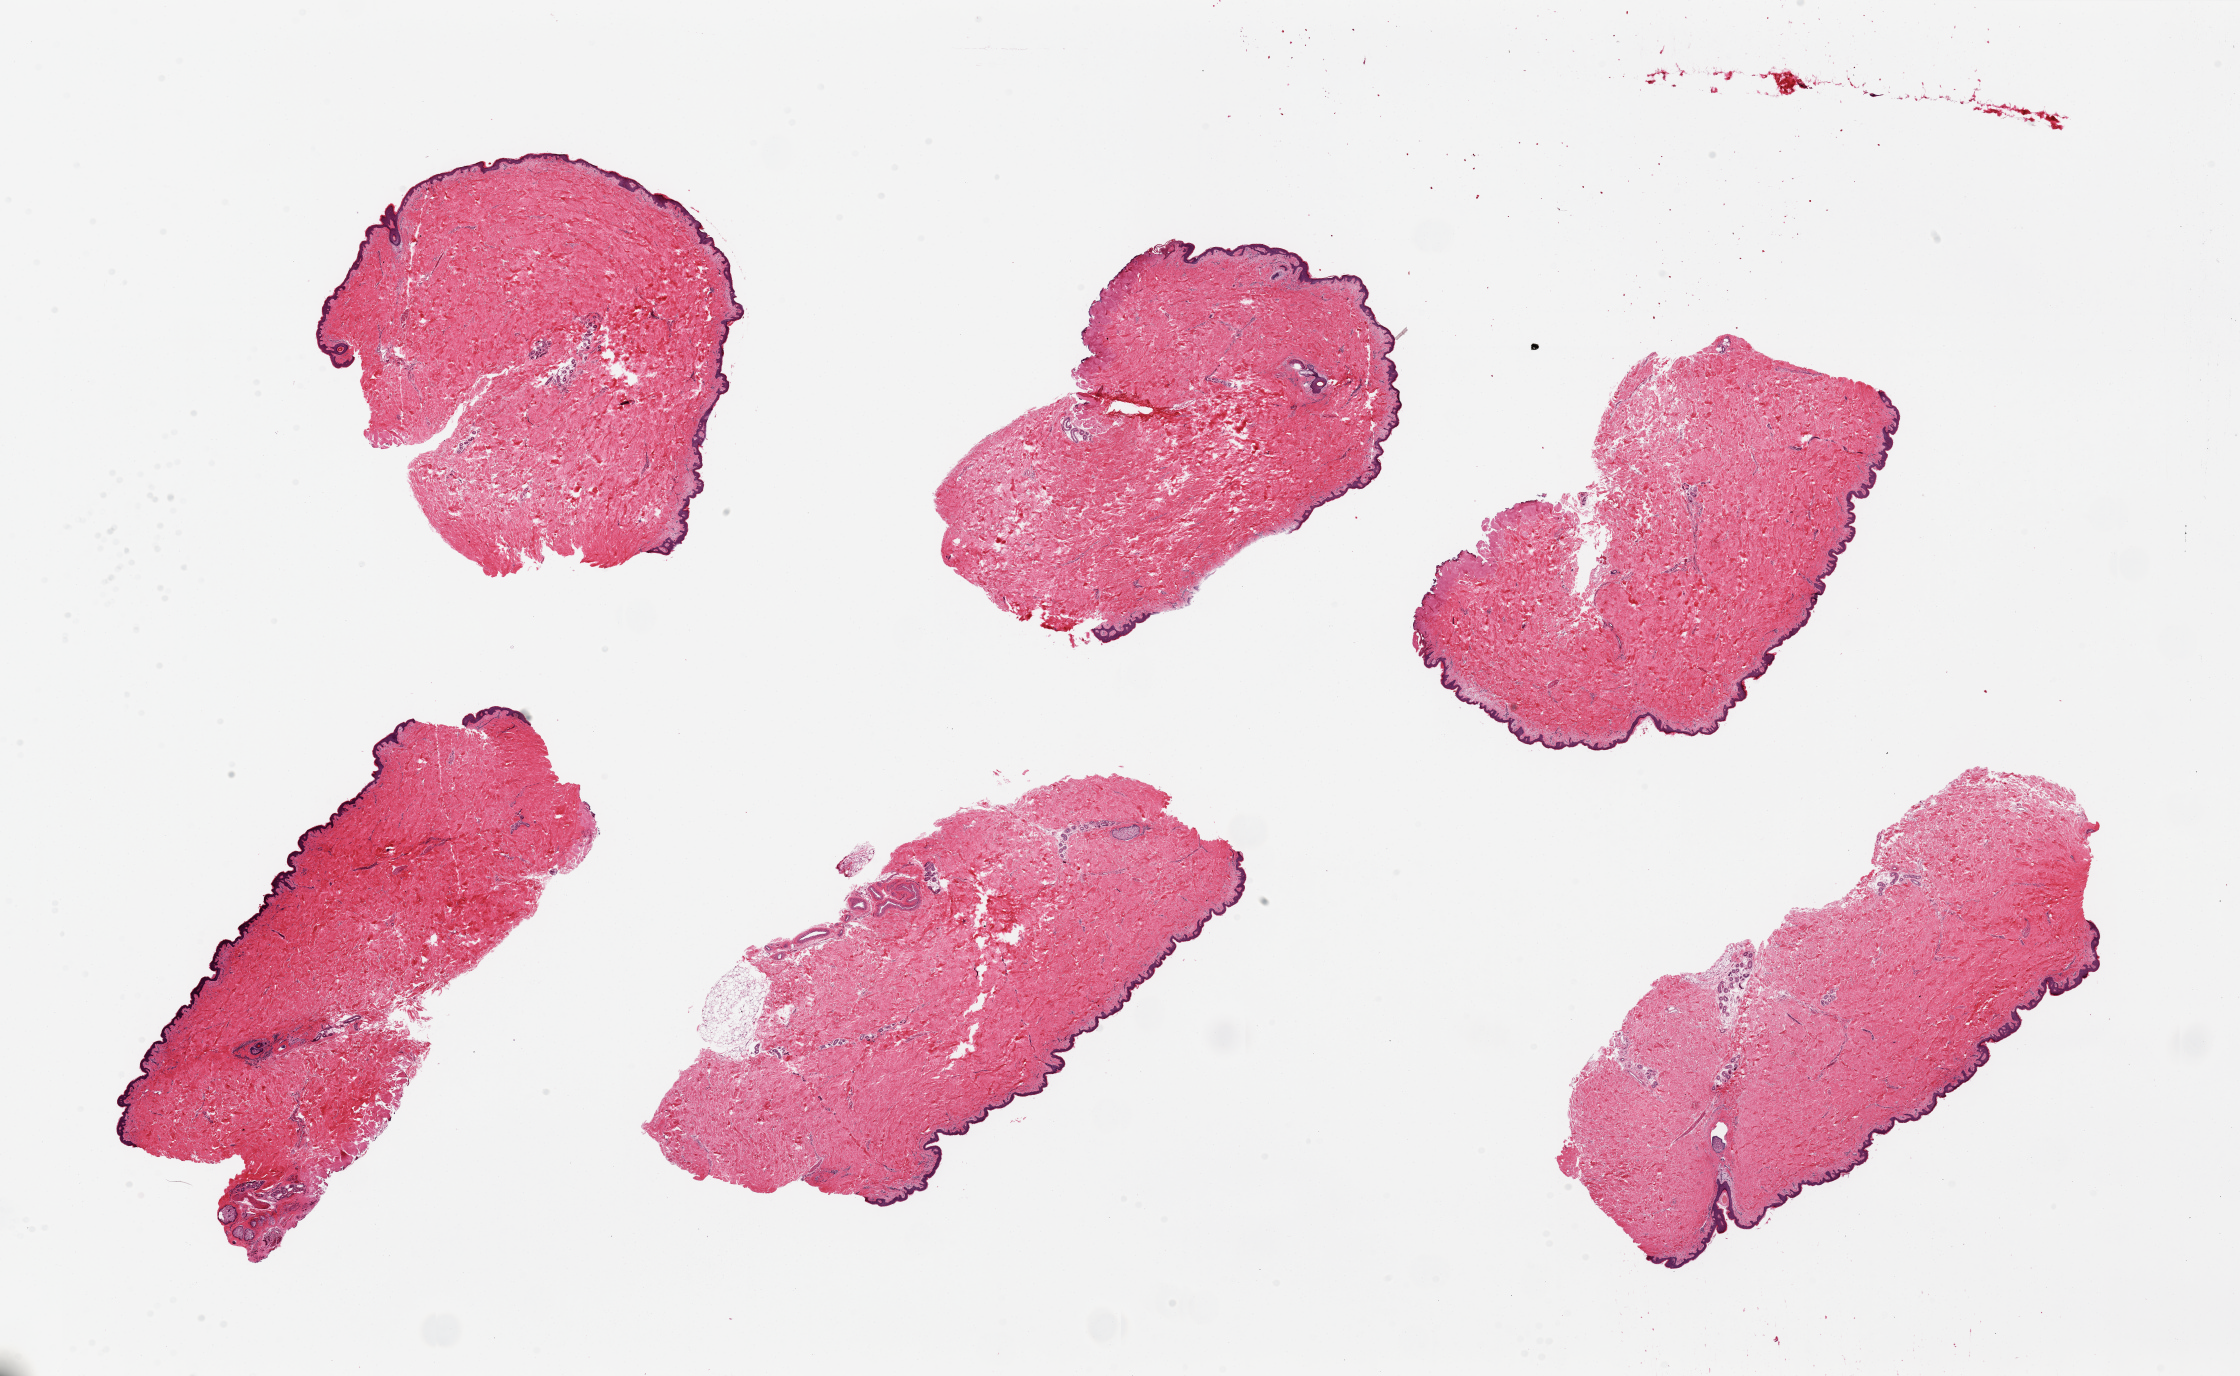
Whole-slide image, H&E stain, brightfield, a low-resolution overview of the entire scanned area, about 35.4 x 21.8 mm; PAXgene-fixed, paraffin-embedded tissue; sampled site (target tissue): skin of suprapubic region; tissue donor sample. Male donor.
Review note (as recorded): 6 pieces, up to 10x4mm; squamous epithelium is ~2-3% thickness.